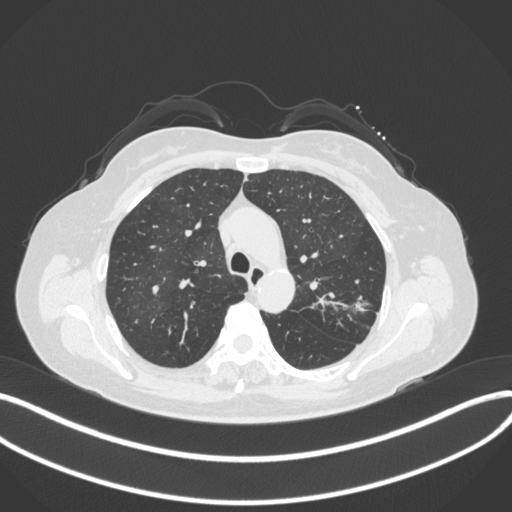
Chest CT, one axial slice. Slice 247 of 330 in the series (ordered by position). Reconstruction kernel B31f. 120 kVp. Lung window (W 1500 / L -600 HU). 1 mm slice thickness. 512 × 512 image matrix. Female patient, age 60 years. Case-level facts recorded for this patient, not image findings: clinical TNM (as recorded): T1c N0 M0.
Annotated regions visible in this slice (rectangle marked by the reading radiologist):
- lung tumour (recorded histology: adenocarcinoma): box from (x=346, y=292) to (x=376, y=318) px